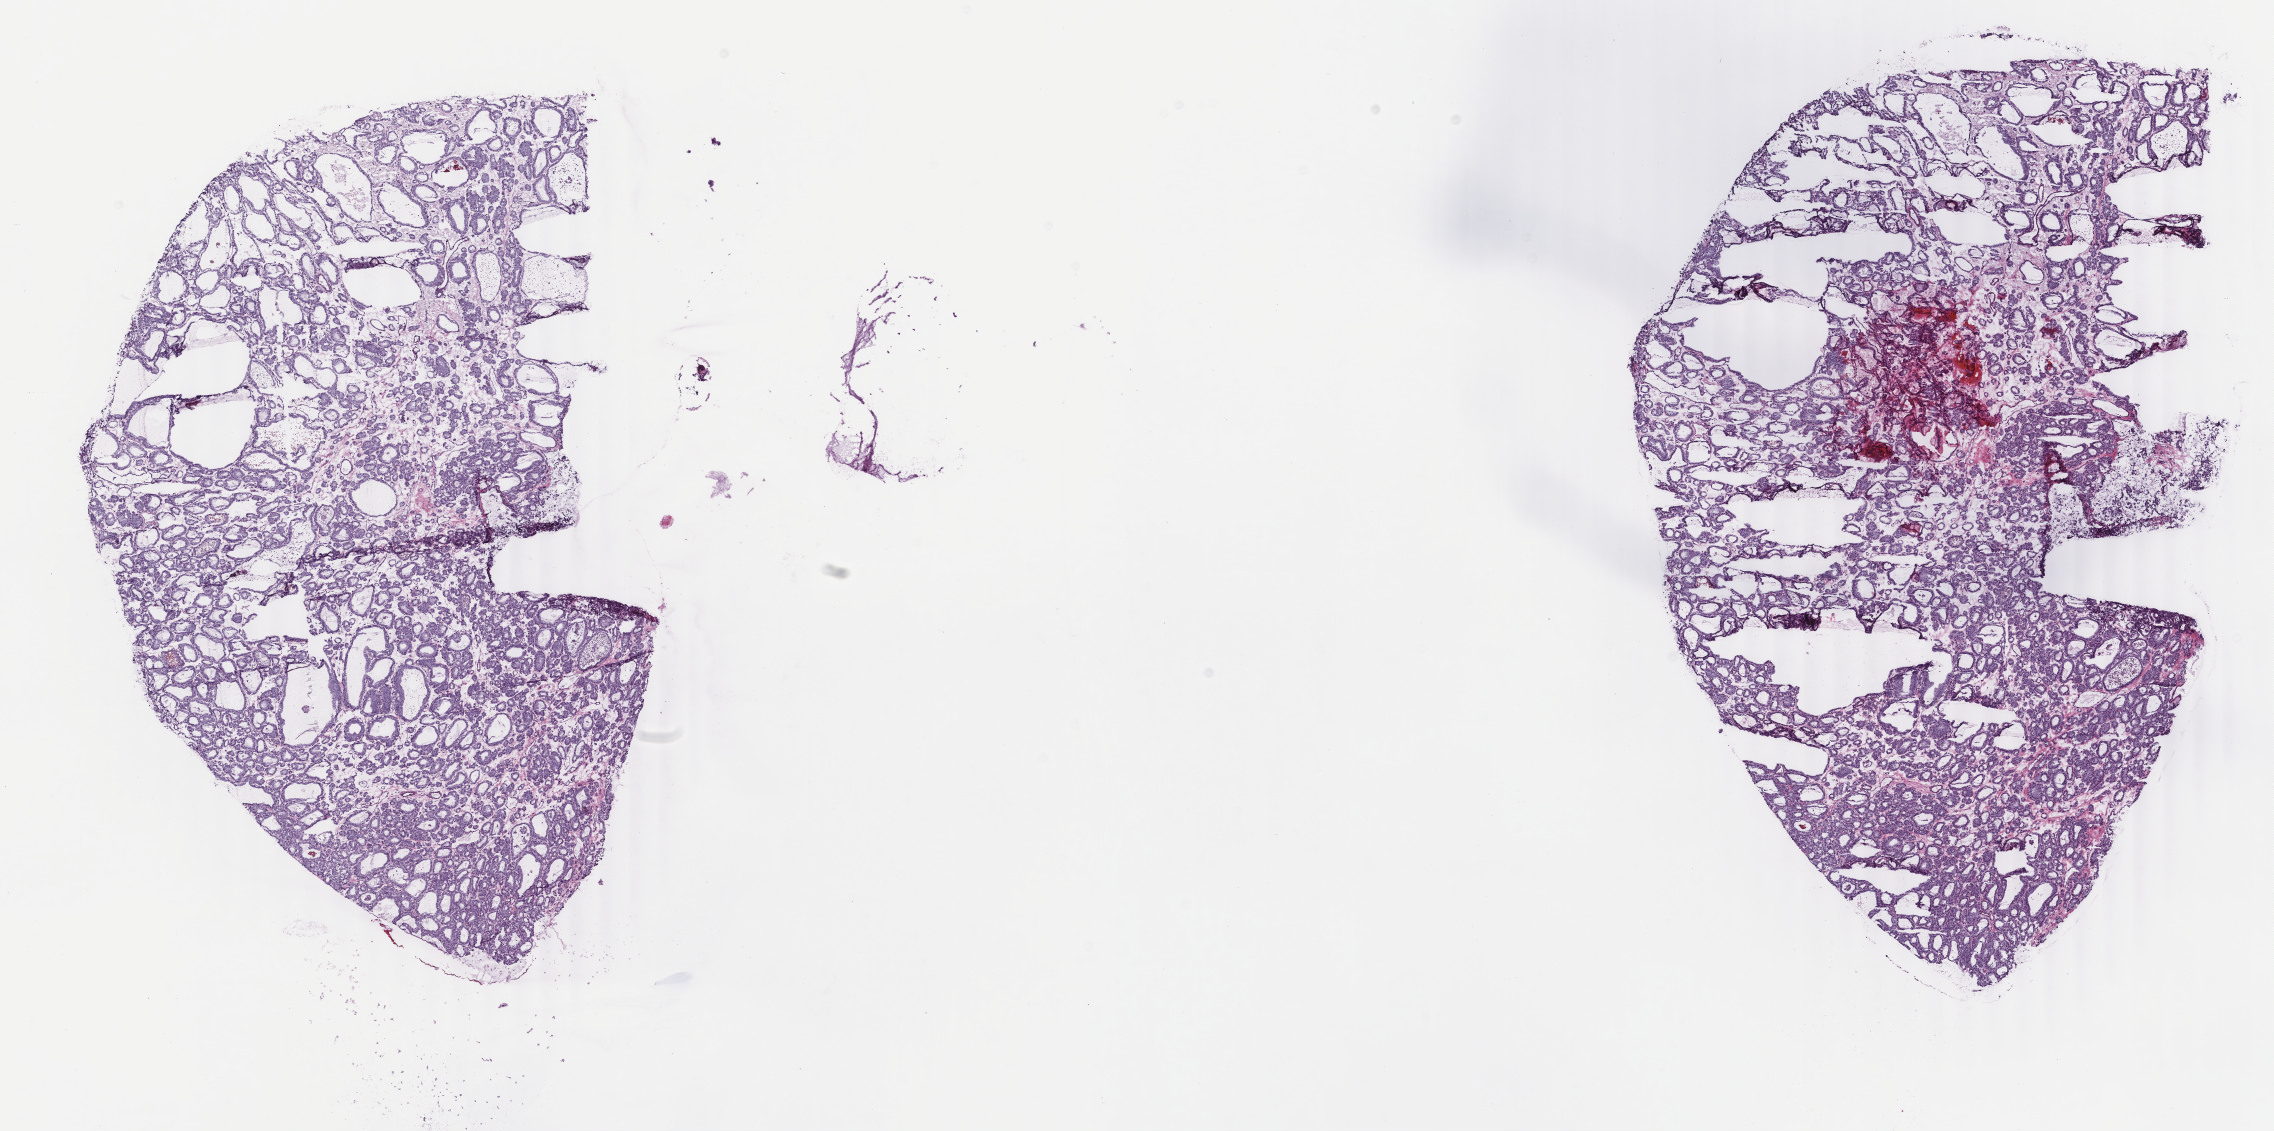
Whole-slide histology image, H&E-stained, a low-resolution overview of the entire scanned area, about 18.1 x 9.0 mm. Frozen section from the top of the tissue portion. Sample: primary tumour, thyroid. Female patient; age at initial diagnosis 33 years. Composition of this section per pathologist review: tumour cells 100%, tumour nuclei 85%, normal cells 0%, stromal cells 0%, necrosis 0%. Infiltration values recorded for this section: lymphocyte infiltration 0%, monocyte infiltration 0%, neutrophil infiltration 0%.
AJCC pathologic stage: I (7th edition). Diagnosis: Papillary carcinoma, follicular variant (thyroid gland). Lymph nodes positive (case pathology): 0 of 1 examined.